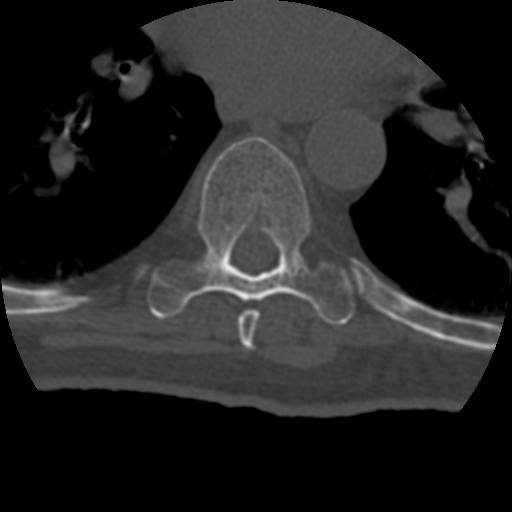
CT including the spine, one axial slice; position 263 of 399 along the scan axis; 120 kVp; bone window (W 1800 / L 400 HU); 1.25 mm slice thickness; 512 × 512 image matrix, field of view 160 × 160 mm. Patient age 69 years. Case-level facts recorded for this patient, not image findings: primary cancer: prostate.
Structures marked on this image (semi-automatically segmented with operator editing):
- T7 vertebra: bounding box <238,309,260,350> (left, top, right, bottom; pixels)
- T8 vertebra: <147,136,359,325>